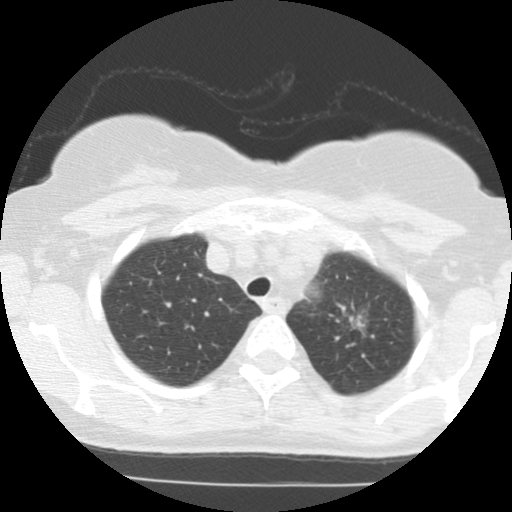
Low-dose screening chest CT, one axial slice. Slice 99 of 123 in the series (ordered by position). Reconstruction kernel STANDARD. 140 kVp. Lung window (W 1500 / L -600 HU). 2.5 mm slice thickness. 512 × 512 image matrix, field of view 290 × 290 mm.
Annotated regions visible in this slice (manually delineated by an expert):
- lesion 1 (tumor, upper lobe of left lung): box from (x=349, y=315) to (x=365, y=330) px